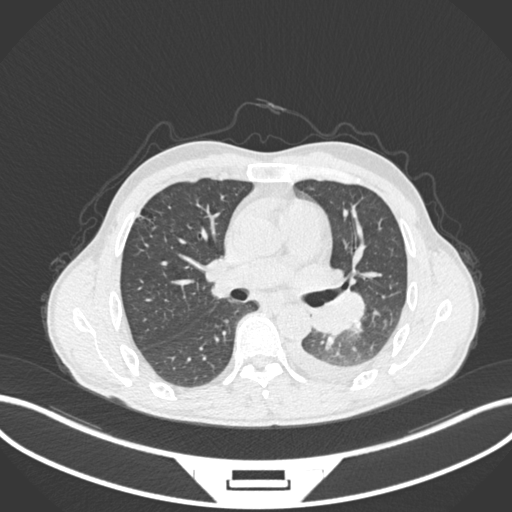
Chest CT, one axial slice. Position 139 of 222 along the scan axis. Reconstruction kernel B30f. Lung window (W 1500 / L -600 HU). 512 × 512 image matrix, field of view 400 × 400 mm. Patient: male, 47 years. From the clinical record (not read from this slice): clinical TNM (as recorded): T3 N1 M1c.
Structures marked on this image (rectangle marked by the reading radiologist):
- lung tumour (recorded histology: small cell carcinoma): bounding box <306,287,366,335> (left, top, right, bottom; pixels)